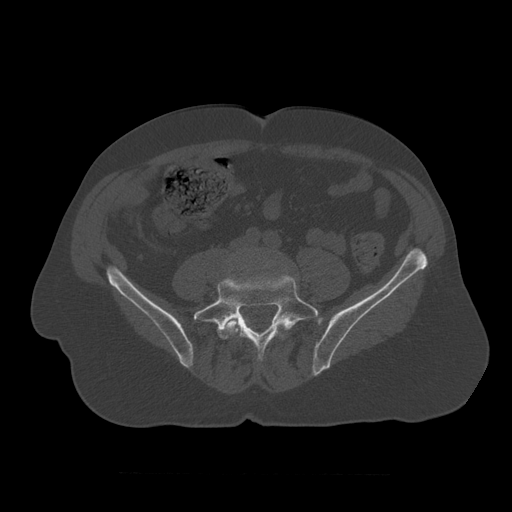
CT including the spine, one axial slice; position 260 of 450 along the scan axis; reconstruction kernel STANDARD; 120 kVp; bone window (W 1800 / L 400 HU); 1.25 mm slice thickness; 512 × 512 image matrix, field of view 405 × 405 mm. Patient age 75 years. From the clinical record (not read from this slice): primary cancer: prostate.
Annotated regions visible in this slice (semi-automatically segmented with operator editing):
- L4 vertebra: box from (x=223, y=278) to (x=293, y=346) px
- L5 vertebra: (x=194, y=273)–(x=319, y=361)